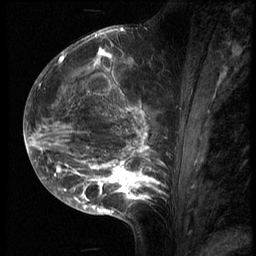
Breast MRI (dynamic contrast-enhanced), one sagittal slice. 3 images stored at this slice position (order not interpretable as contrast timing). 1.5 T. TE 4.2 ms, TR 9 ms. 2.5 mm slice thickness. 256 × 256 image matrix, field of view 180 × 180 mm. Female patient, age 28 years. From the clinical record (not read from this slice): setting: breast cancer imaged before/during neoadjuvant chemotherapy.
Structures marked on this image (semi-automatically segmented with operator editing):
- analysis volume of interest (the breast-tissue region the enhancement analysis was run in; not a lesion): box from (x=43, y=42) to (x=185, y=215) px
- tumour enhancement mask (voxels above the 140 % enhancement threshold inside the analysis volume of interest): (x=43, y=48)–(x=166, y=213)